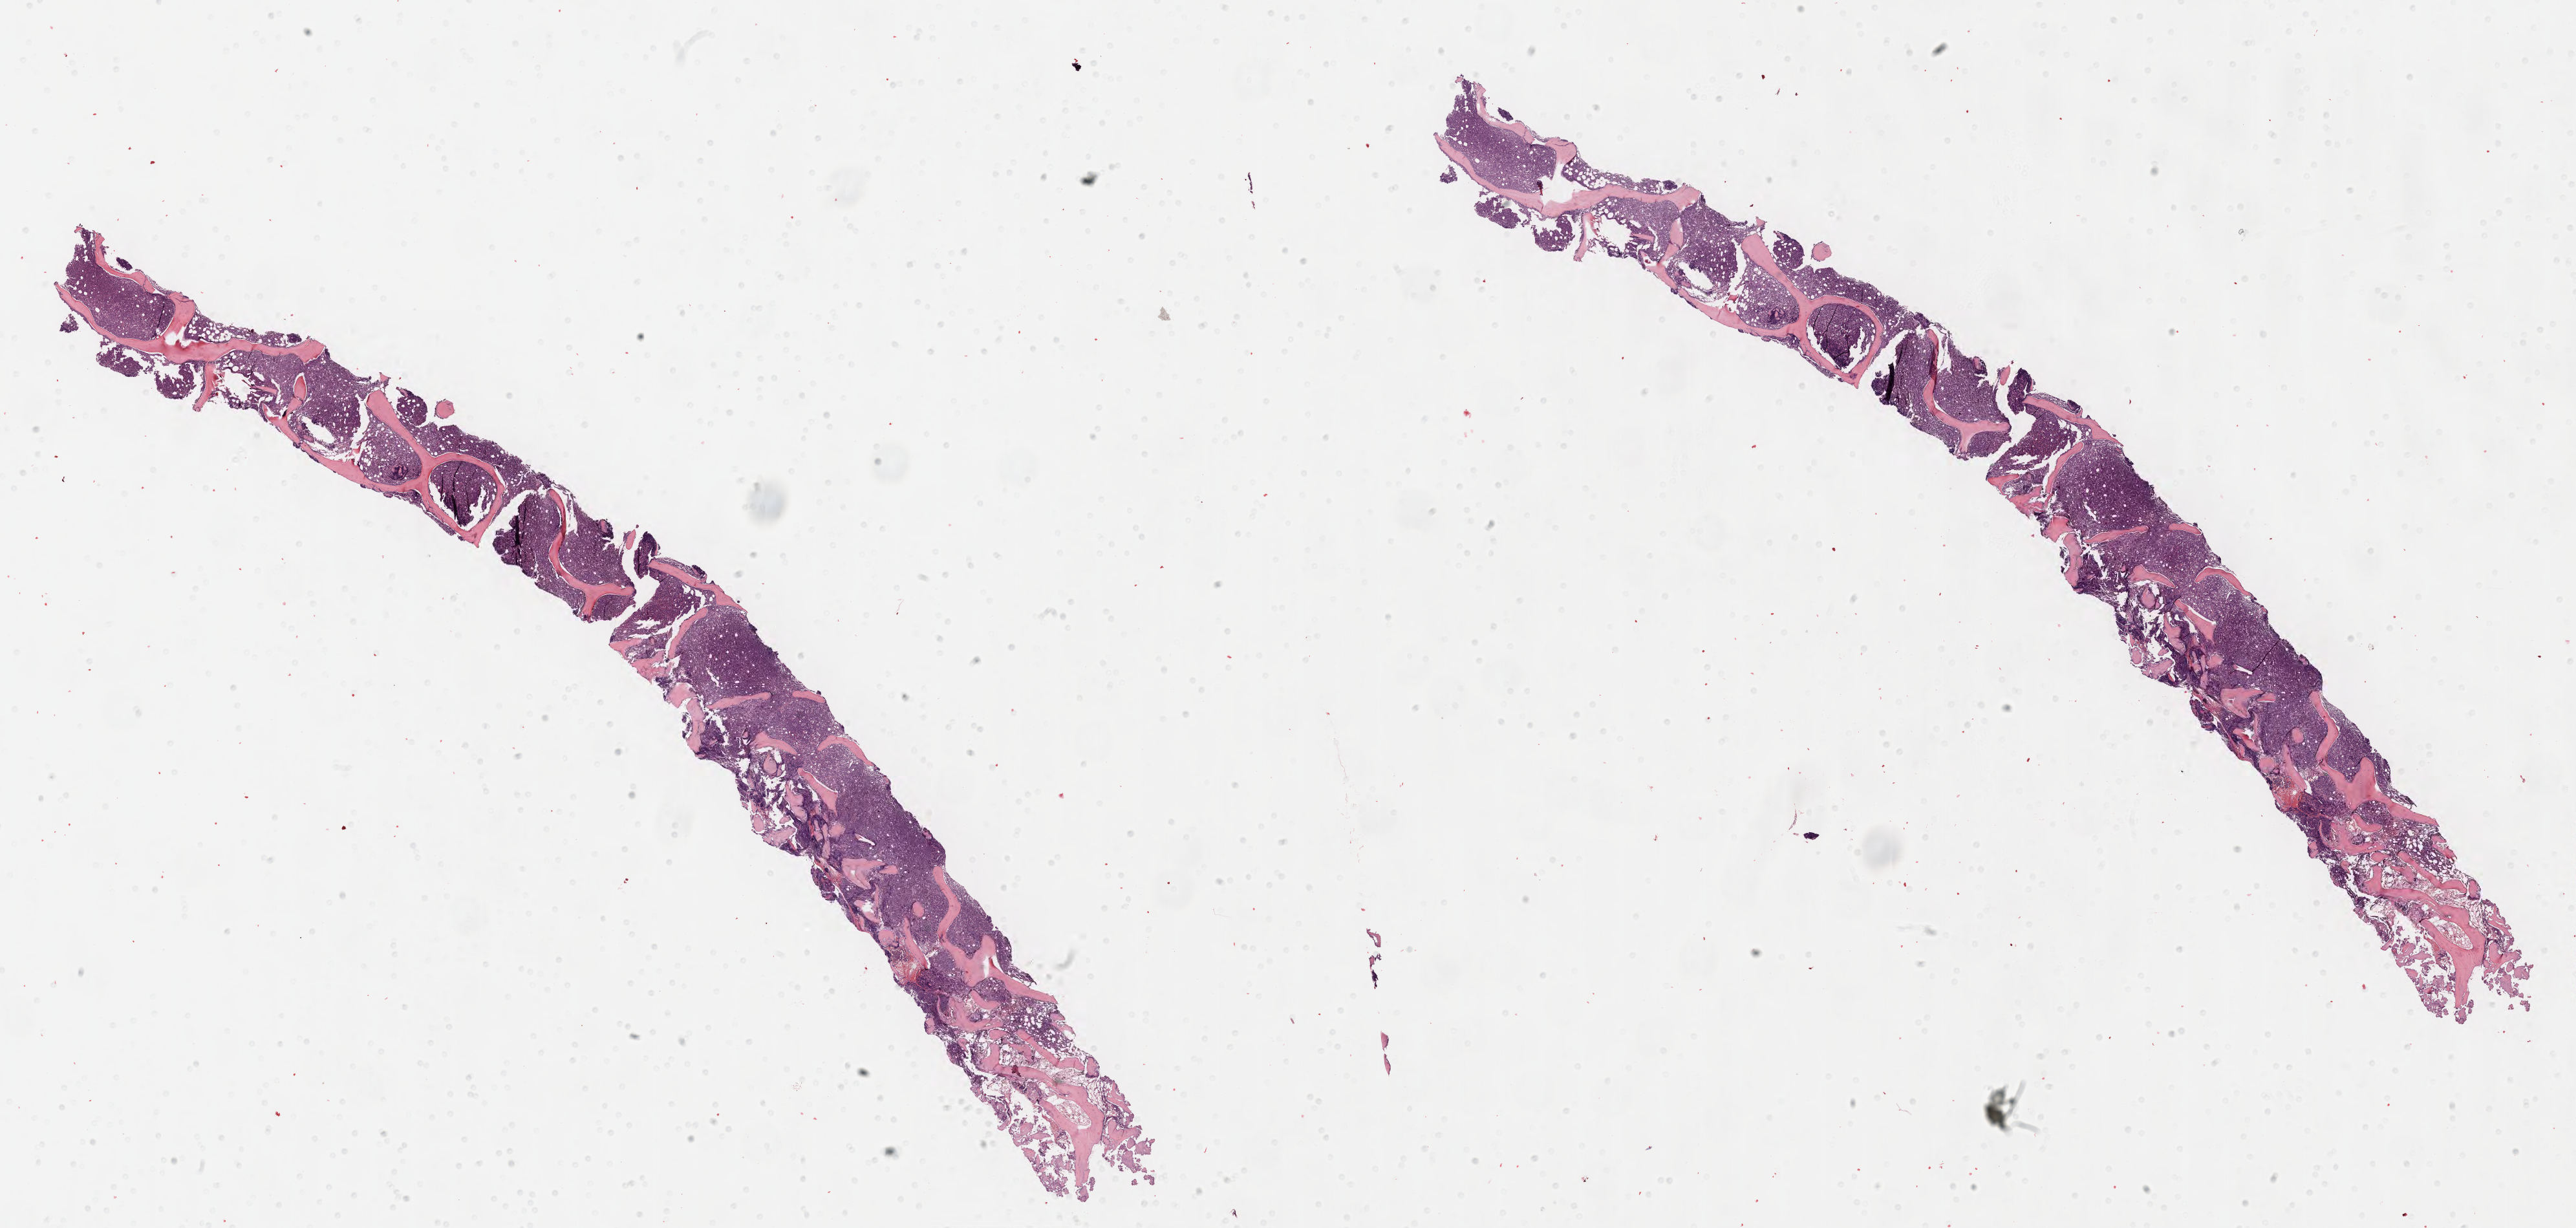
Digitized H&E-stained section, low-resolution overview of the scanned area, about 32.2 x 15.3 mm; specimen: tumor tissue. Male patient.
Diagnosis: Burkitt lymphoma, NOS.